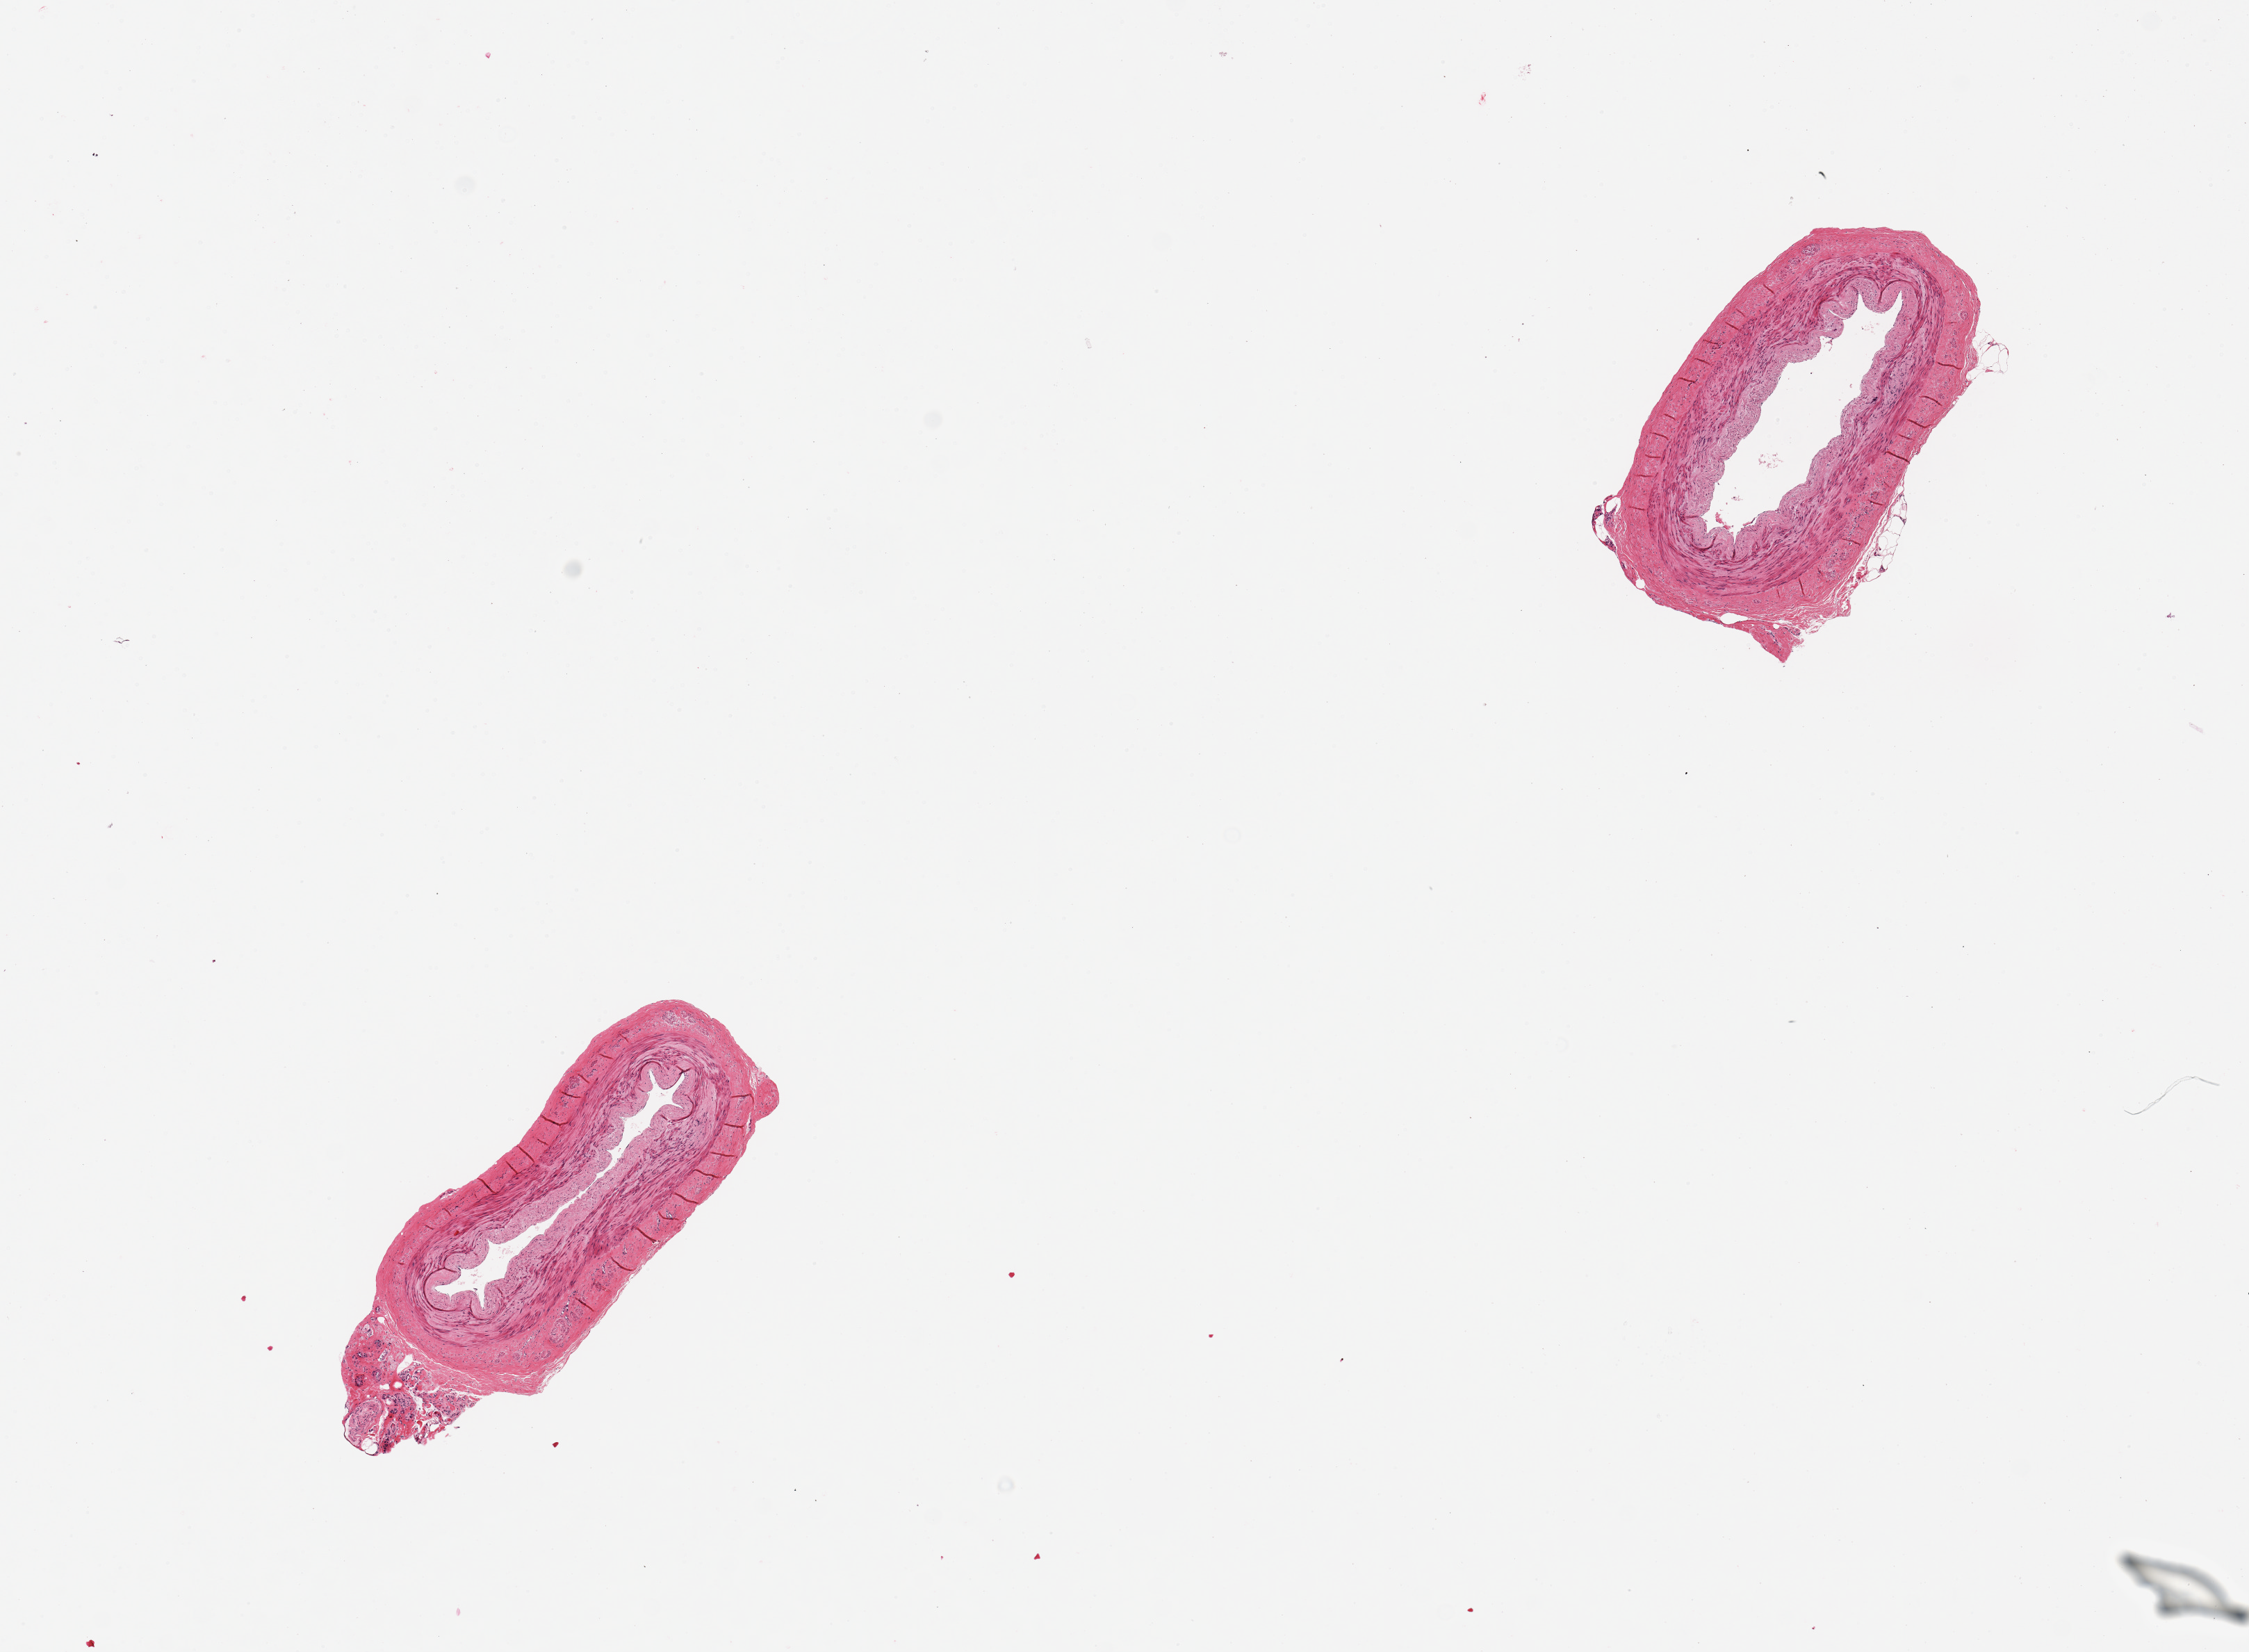
Digitized haematoxylin and eosin-stained section, low-resolution overview of the scanned area, about 12.8 x 9.4 mm (slide scanned at 20x). Donor sex: female.
• specimen: PAXgene-fixed, paraffin-embedded tissue; sampled site (target tissue): tibial artery; donor tissue sample